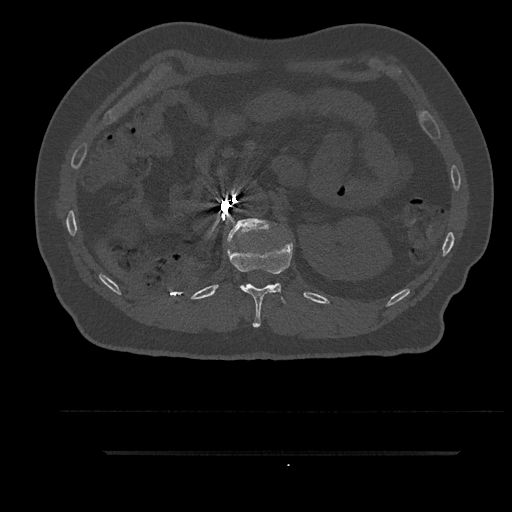
CT including the spine, one axial slice. Slice 224 of 797 in the series (ordered by position). 120 kVp. Bone window (W 1800 / L 400 HU). 0.5 mm slice thickness. 512 × 512 image matrix. Male patient, age 63 years. From the clinical record (not read from this slice): primary cancer: renal; vertebrae with lytic lesions (as recorded): T8.
Structures marked on this image (semi-automatic segmentation, software-assisted and operator-edited):
- L1 vertebra: box from (x=226, y=216) to (x=271, y=244) px
- T12 vertebra: (x=227, y=229)–(x=293, y=328)